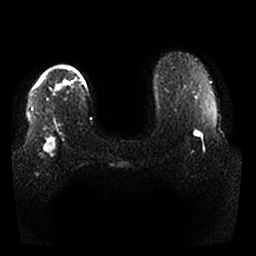
Breast MRI, one axial slice; diffusion-weighted series; image 2 of 4 stored at this slice position (different b-values; order by instance number); 1.5 T; 256 × 256 image matrix, field of view 350 × 350 mm. Female patient.
Structures marked on this image (expert manual segmentation):
- tumour on diffusion-weighted imaging: bounding box <45,136,57,153> (left, top, right, bottom; pixels)